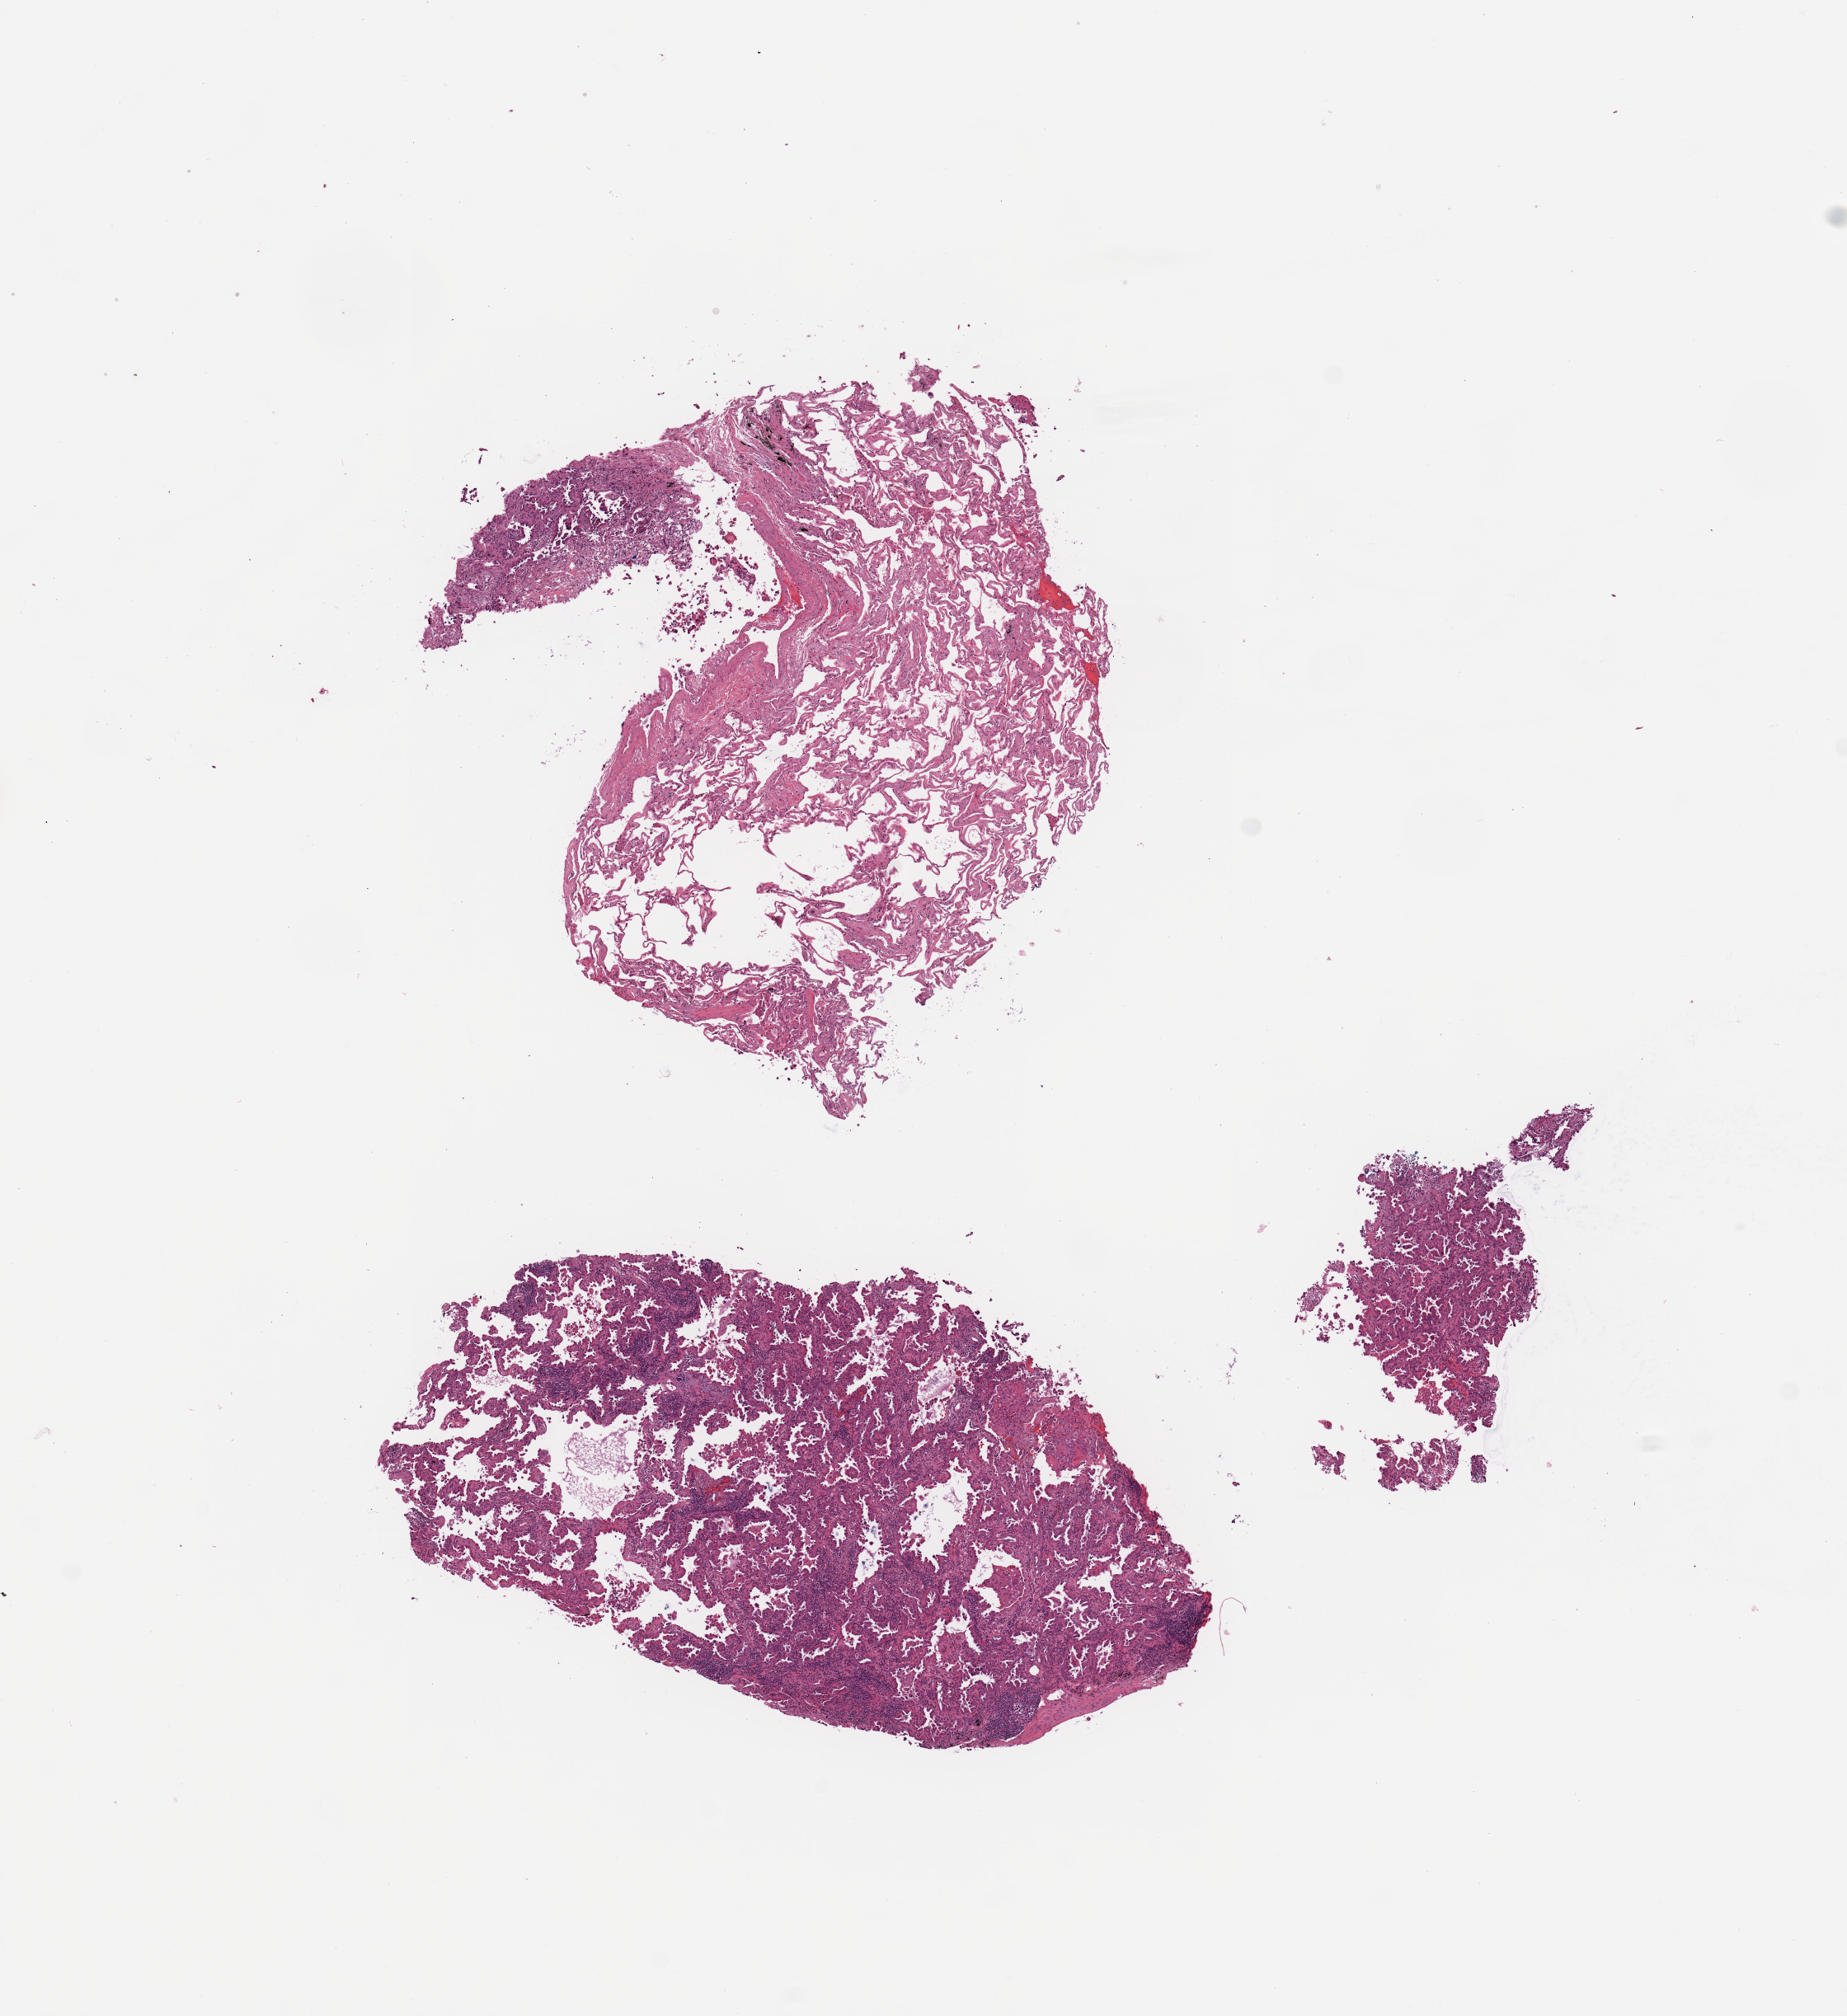
Digitized H&E-stained tissue section (whole slide) — shown as a low-resolution overview of the whole scanned area (about 8.9 x 9.7 mm, acquisition: 20x scan); tumour tissue sample, sampled site: lung. Patient: female, age 68 years. Histologic grade: G2 (moderately differentiated). Slide review estimates, as recorded: tumour nuclei 65%, necrosis 5%.
Primary tumour site (as recorded): right upper lobe. Diagnosis: Adenocarcinoma, NOS. AJCC pathologic stage: IB.